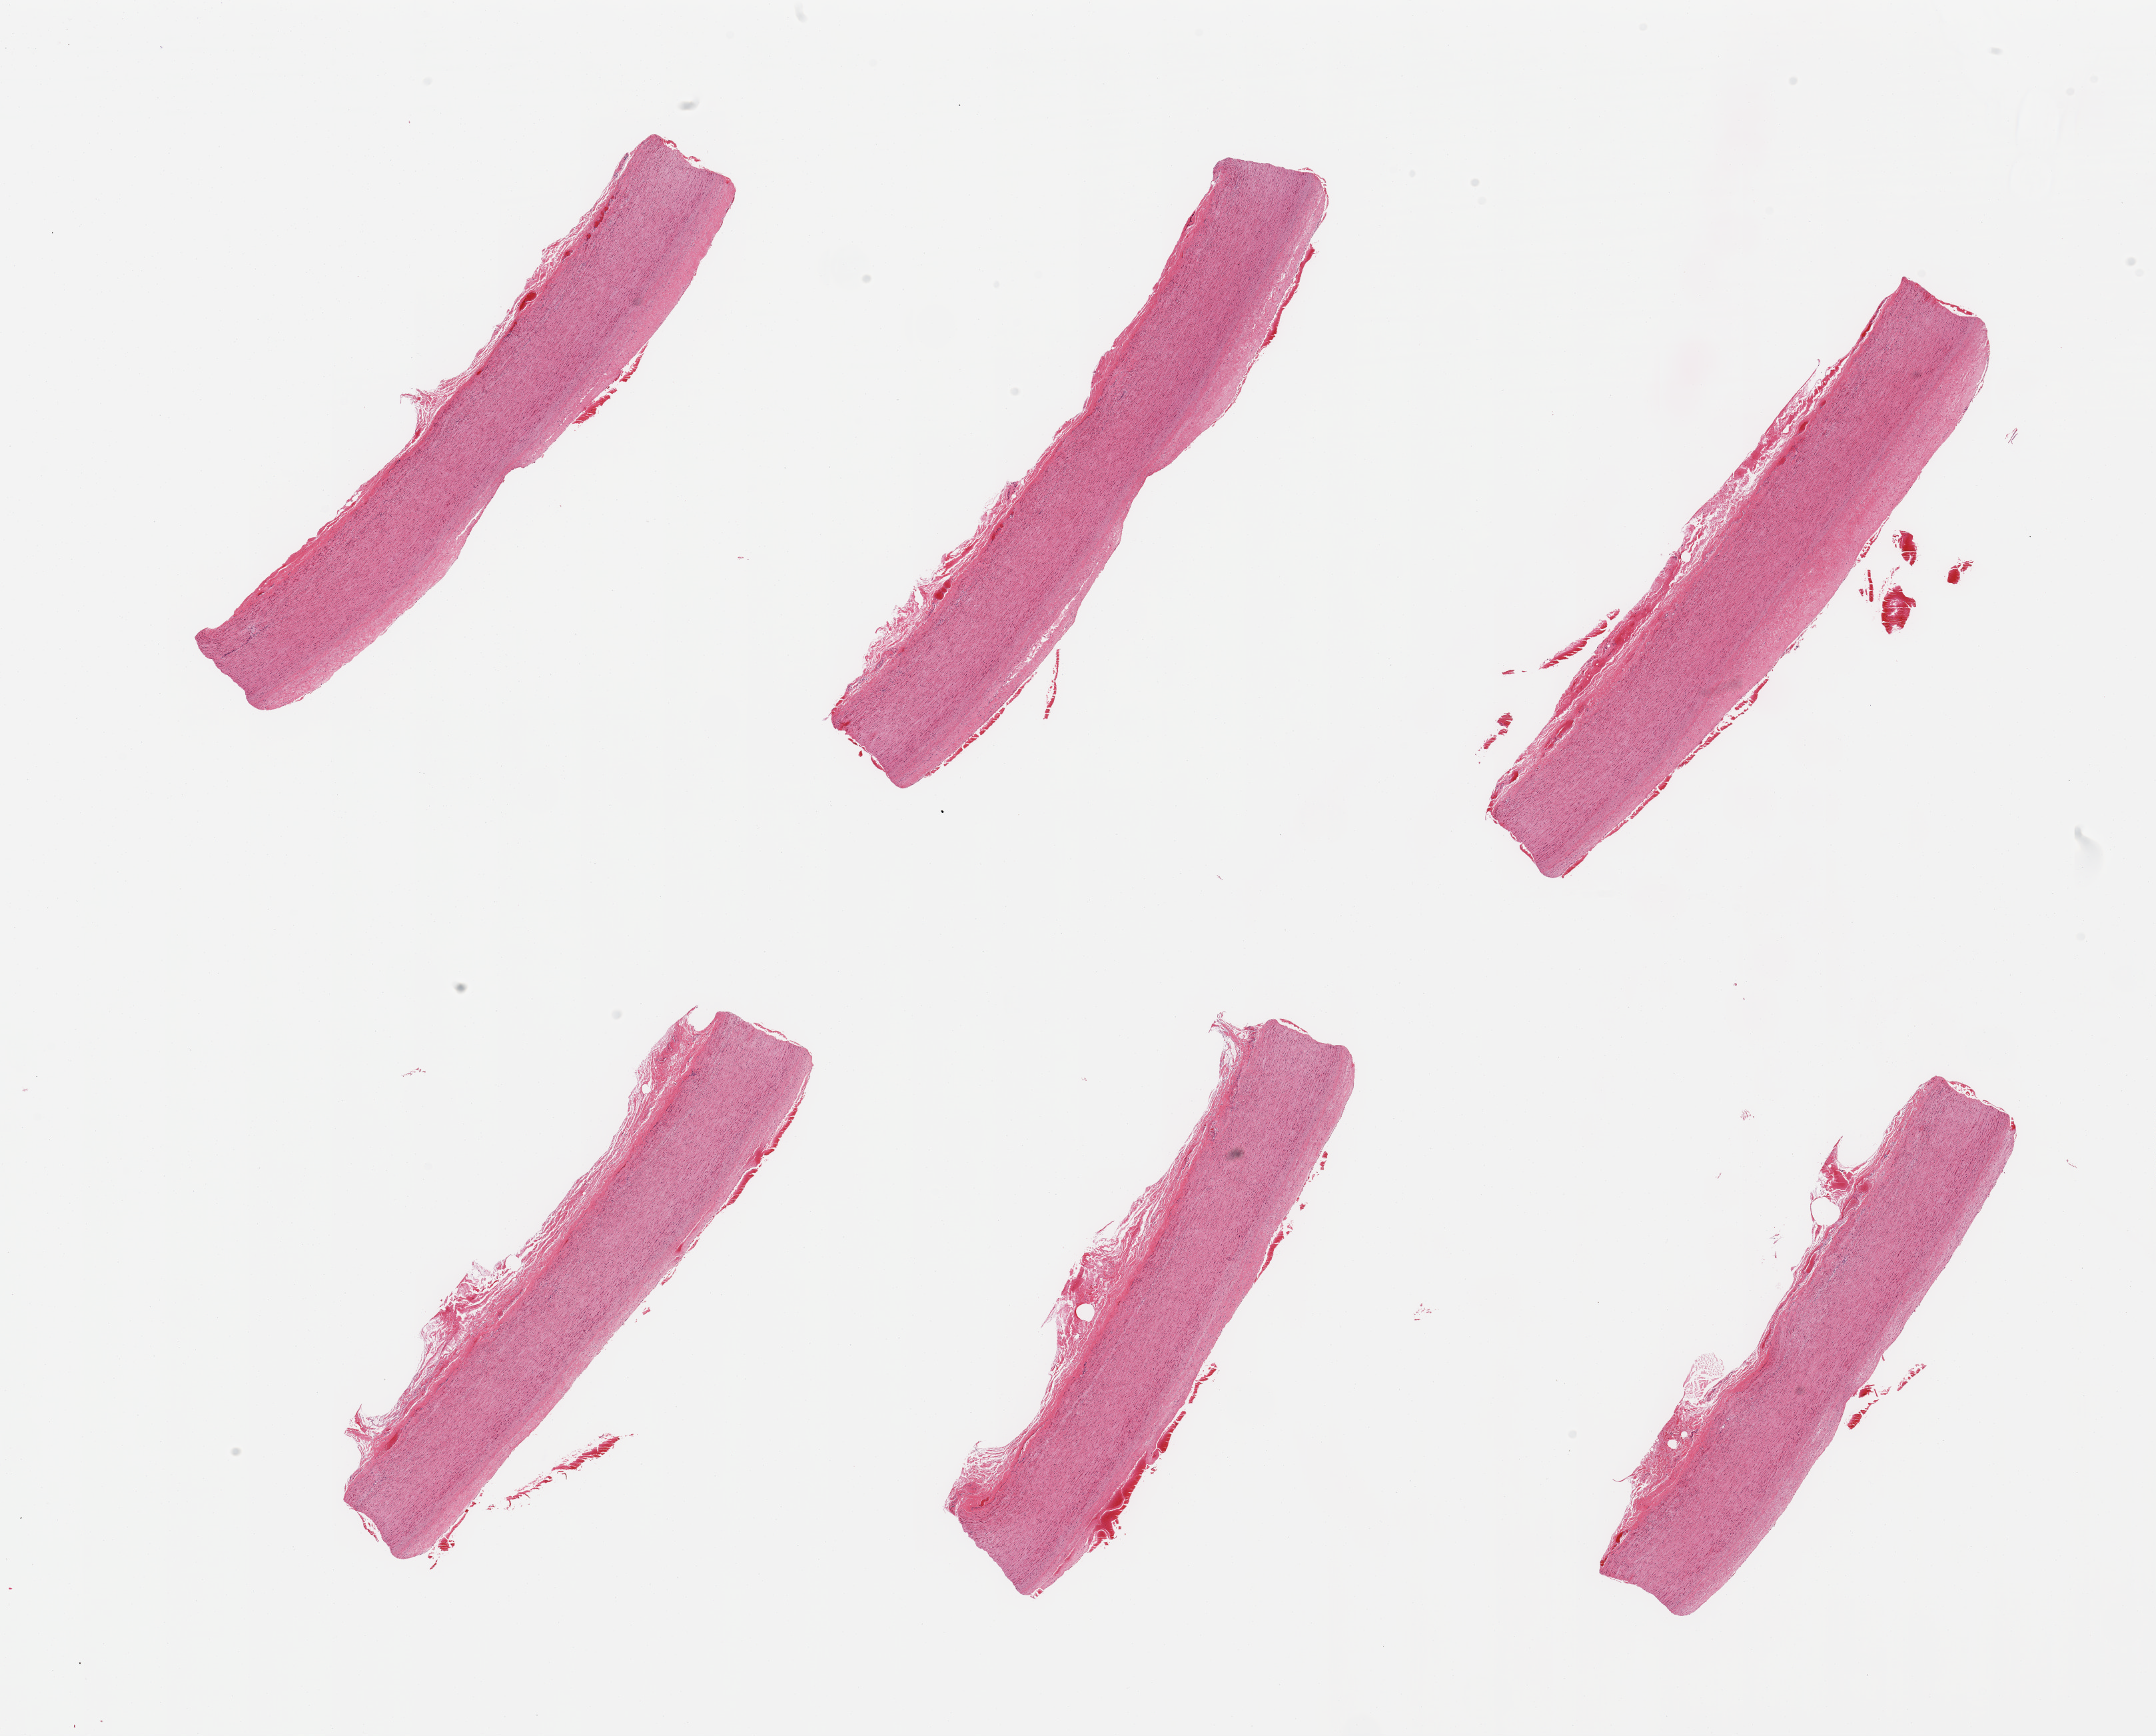
Whole-slide image, haematoxylin and eosin stain, brightfield, low-resolution overview of the scanned area, about 25.6 x 20.6 mm. PAXgene-fixed paraffin-embedded (PFPE) section. Section of aorta (target tissue). Donor tissue sample. Male donor.
Pathologist's review note for this sample: 6 pieces, atherosis up to ~0.3mm.